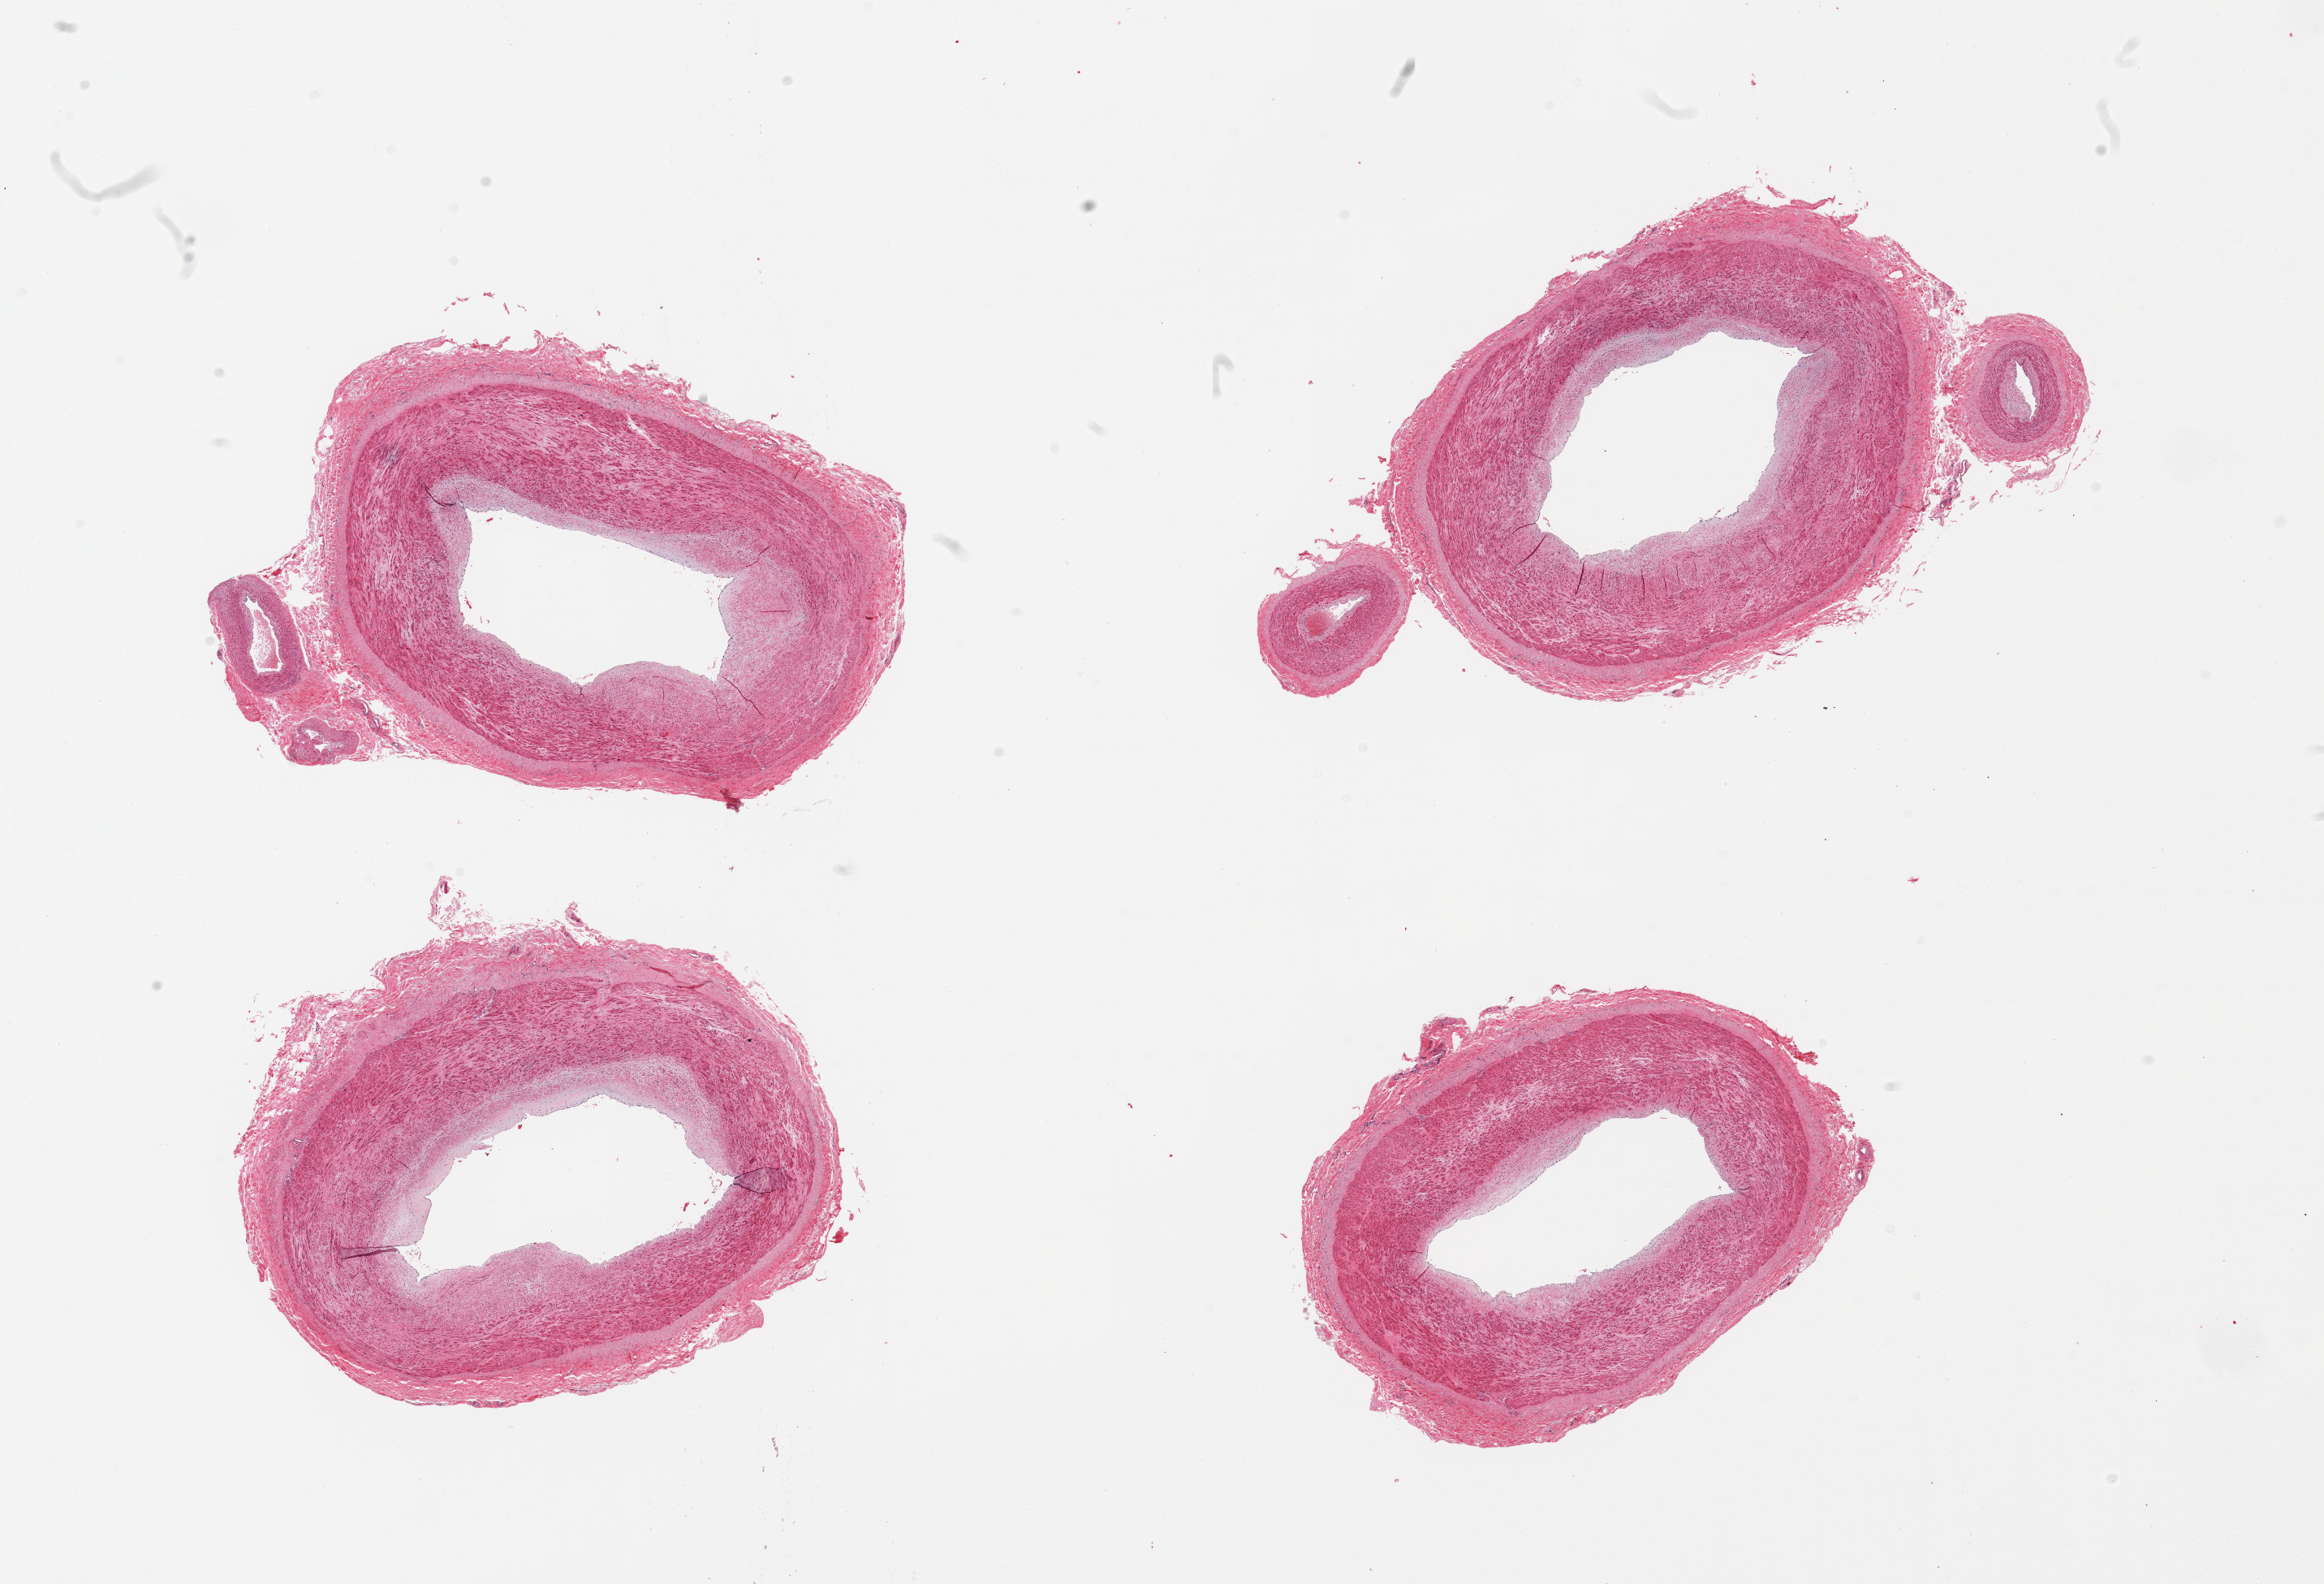
Whole-slide image, haematoxylin and eosin stain — a low-resolution overview of the entire scanned area, about 22.6 x 15.4 mm; PAXgene-fixed paraffin-embedded (PFPE) section; section of tibial artery (target tissue); donor tissue sample.
Reviewer comment on this tissue sample: 4 pieces; mild atherosclerosis.